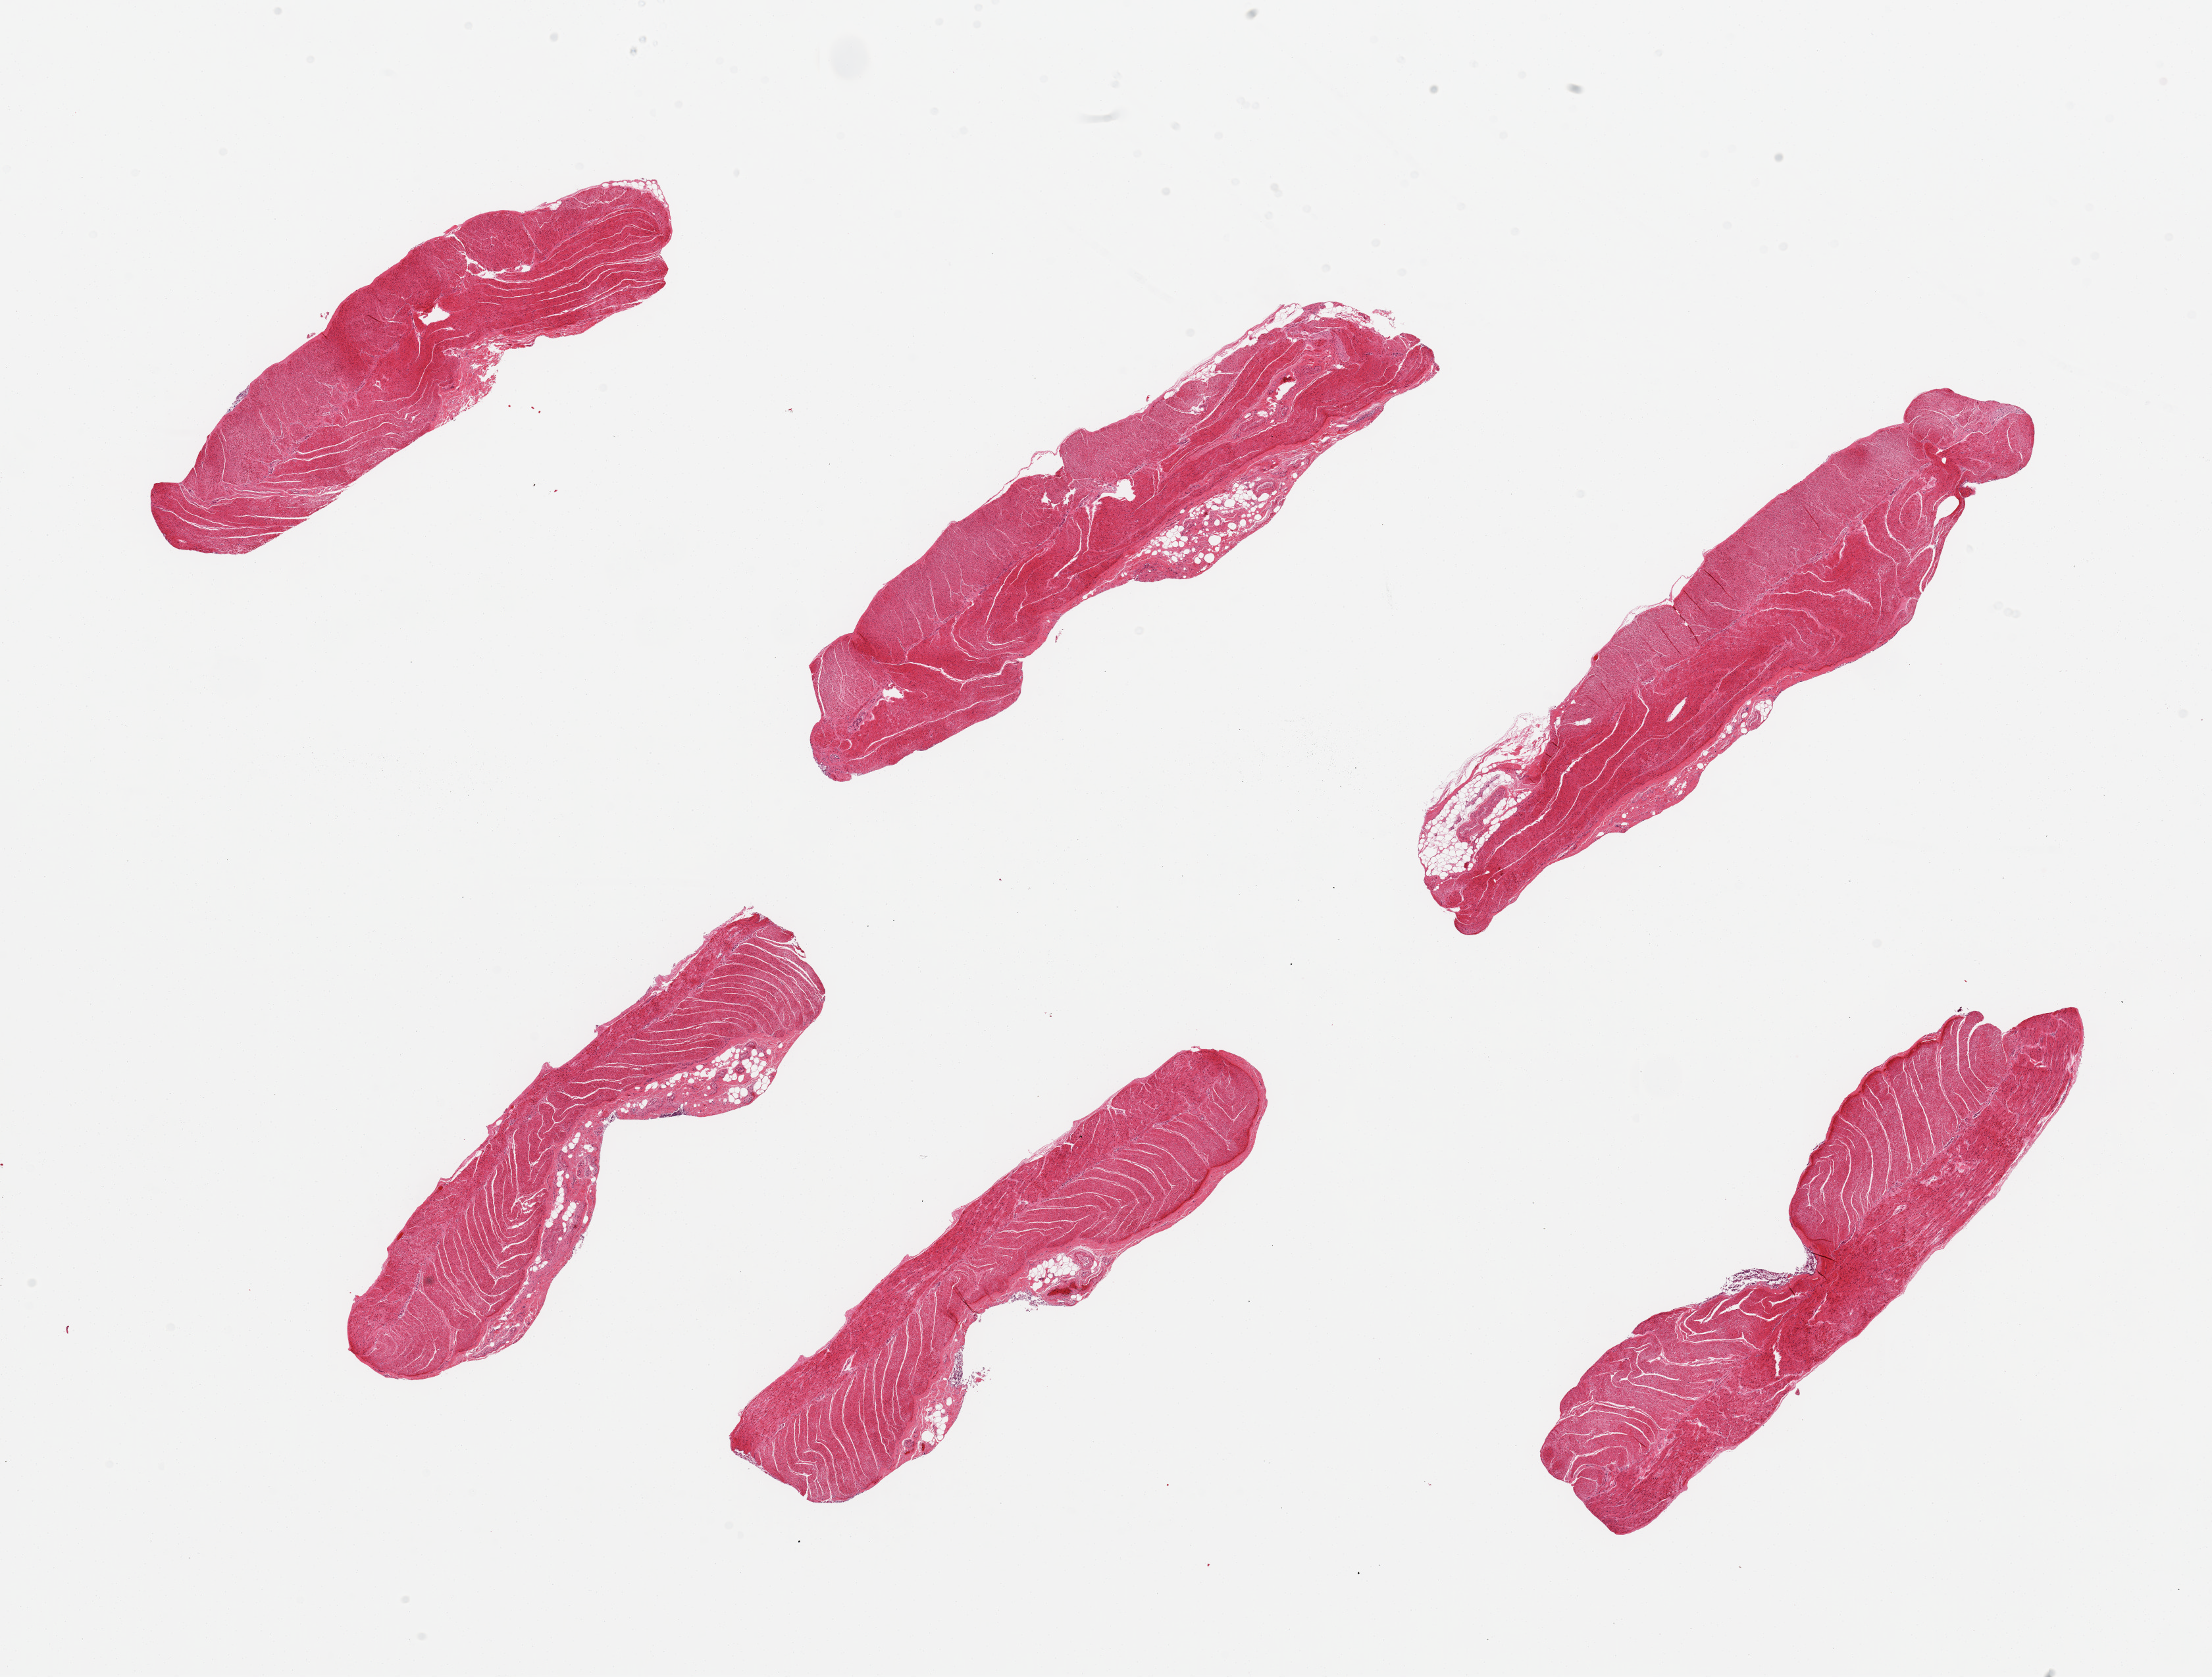
H&E whole-slide image — shown as a low-resolution overview of the whole scanned area (about 26.6 x 20.2 mm), PAXgene-fixed paraffin-embedded (PFPE) section, target tissue: sigmoid colon, tissue donor sample. Donor sex: female.
Review note (as recorded): 6 pieces; muscle with small amounts of external fat.